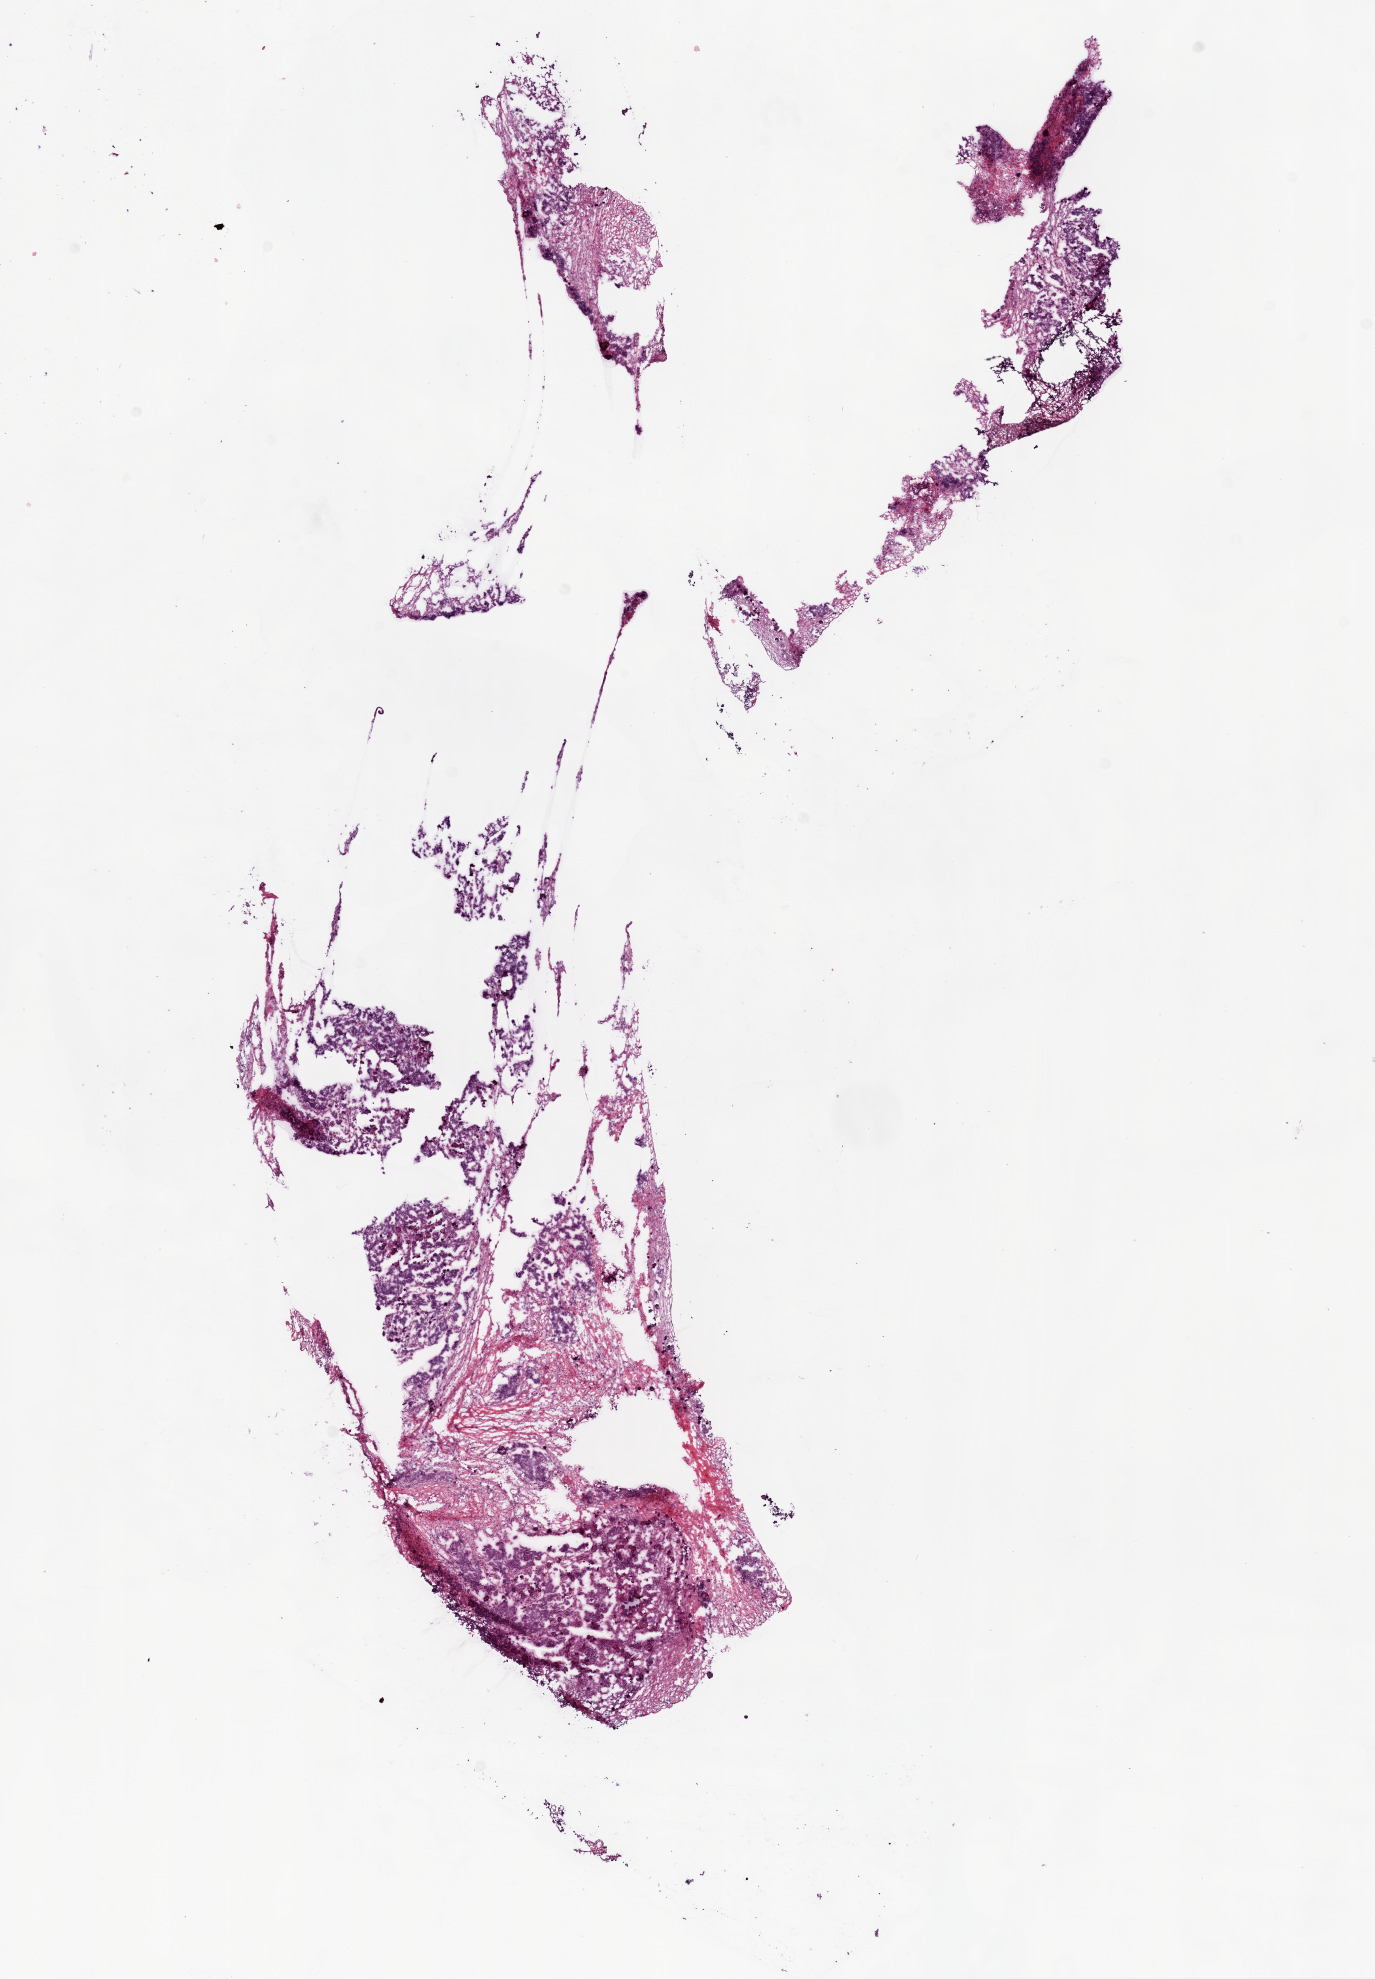
H&E-stained whole-slide image — low-resolution overview of the scanned area, about 11.0 x 15.9 mm (acquisition: 20x scan), frozen section, ovary, primary tumour sample. Female, age 46 years at initial diagnosis. Histologic grade: GX (grade cannot be assessed). Pathologist review of this section (percent, as recorded): tumour cells 70%, tumour nuclei 80%, normal cells 0%, stromal cells 30%, necrosis 0%.
Diagnosis: Serous cystadenocarcinoma, NOS. FIGO stage: IV.